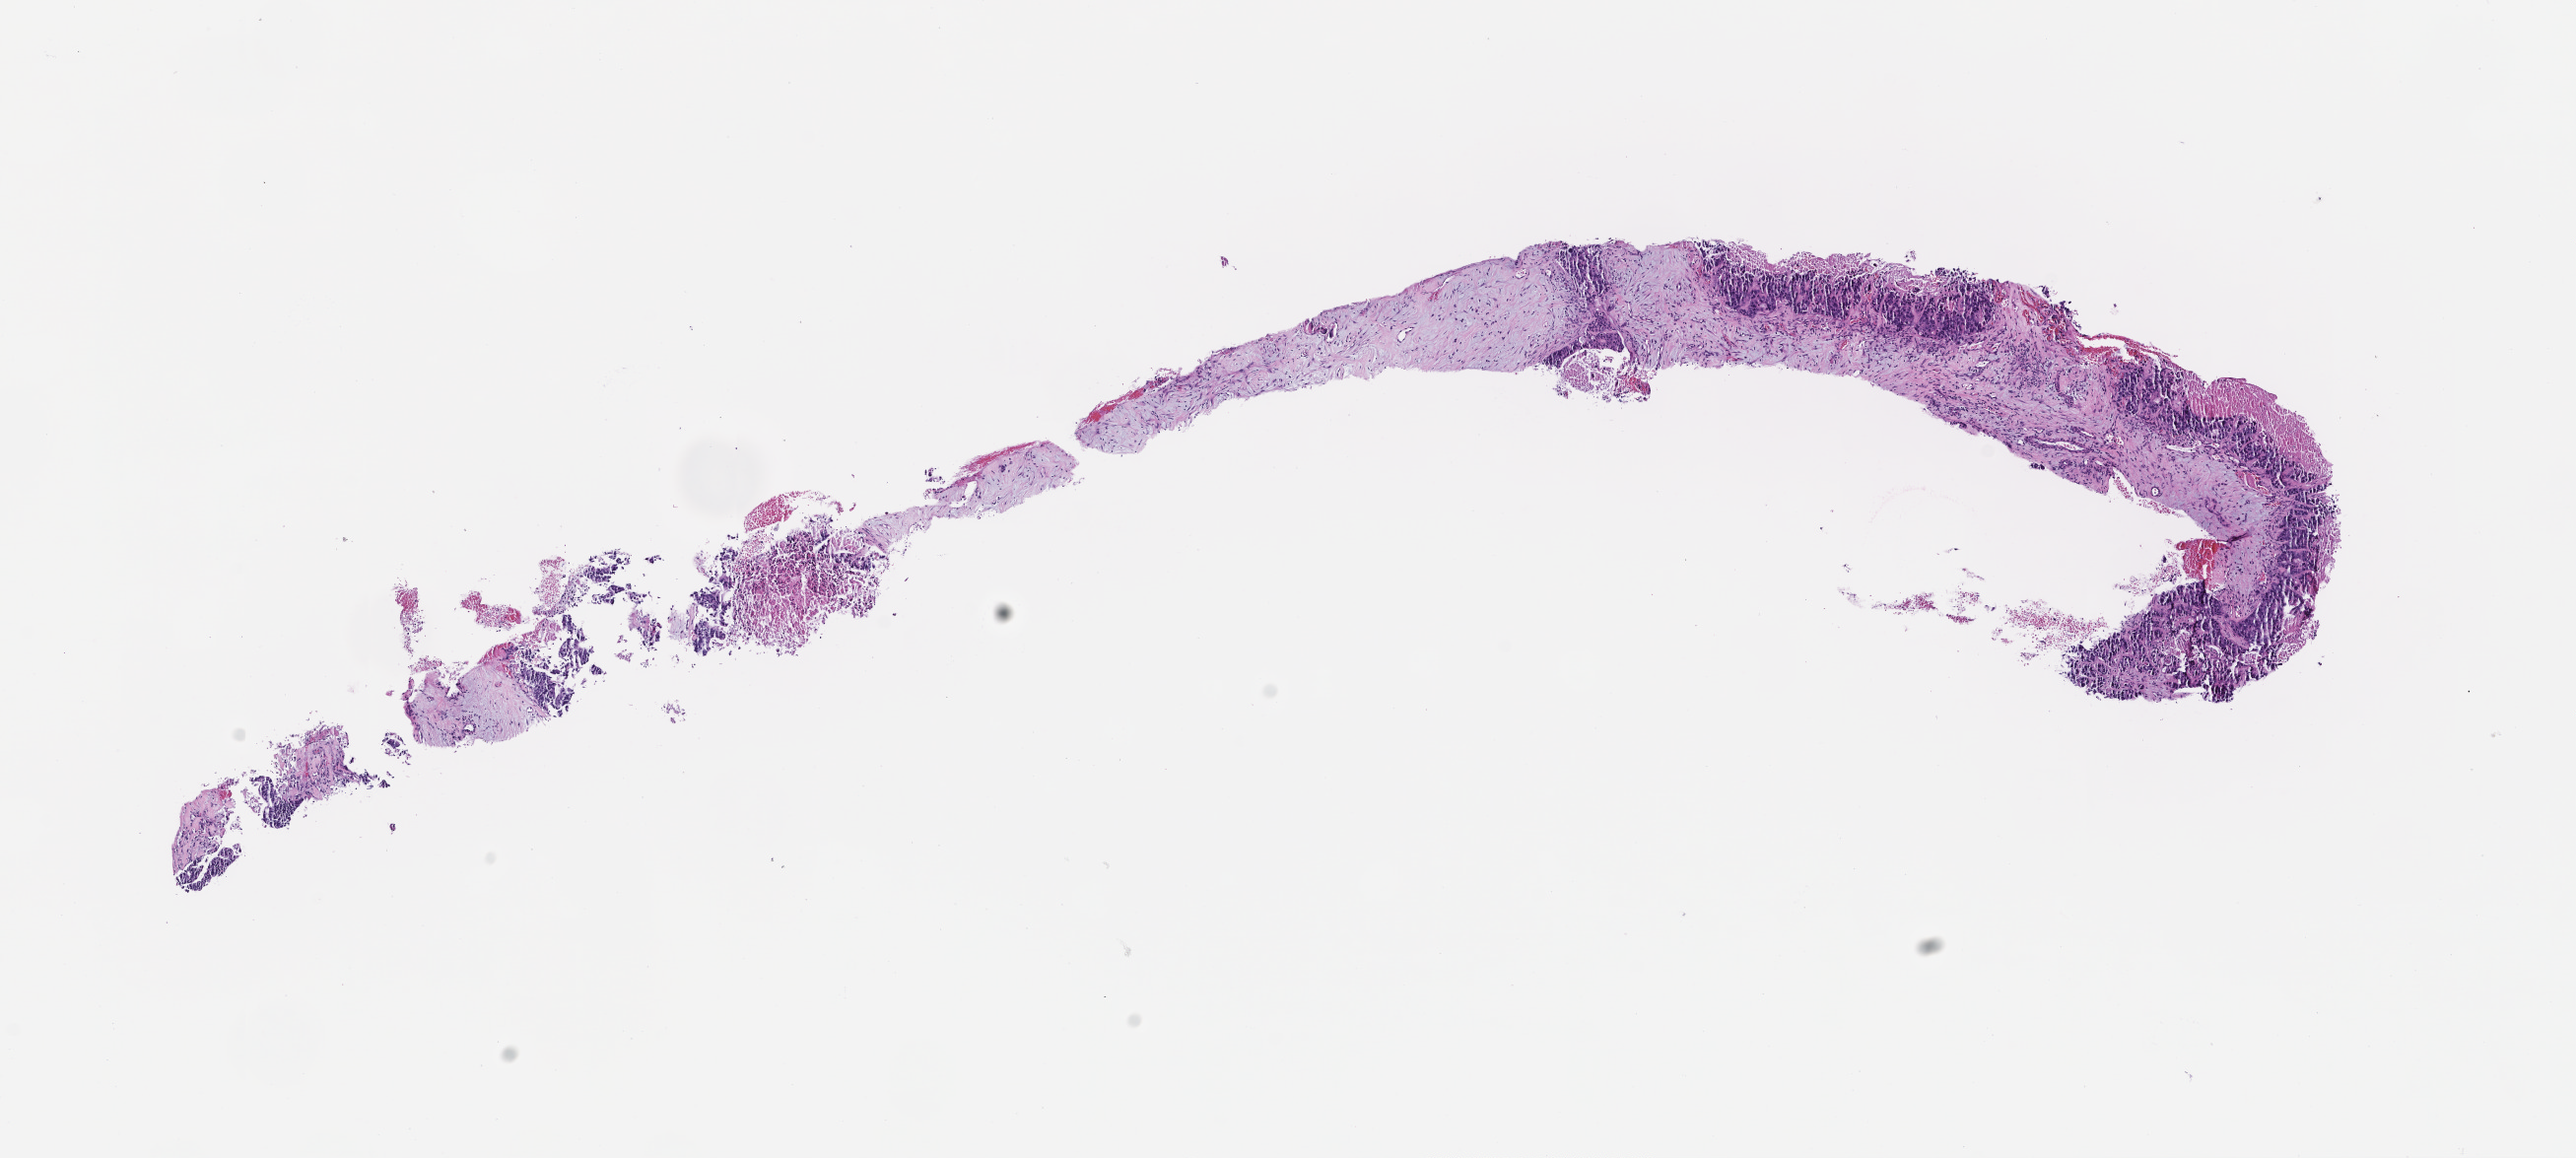
Haematoxylin and eosin whole-slide image — whole scanned area (about 10.6 x 4.7 mm) shown as a low-resolution overview, FFPE section. Female patient.
This section: metastasis (sampled organ not recorded). Patient diagnosis (primary): Colorectal Carcinoma.